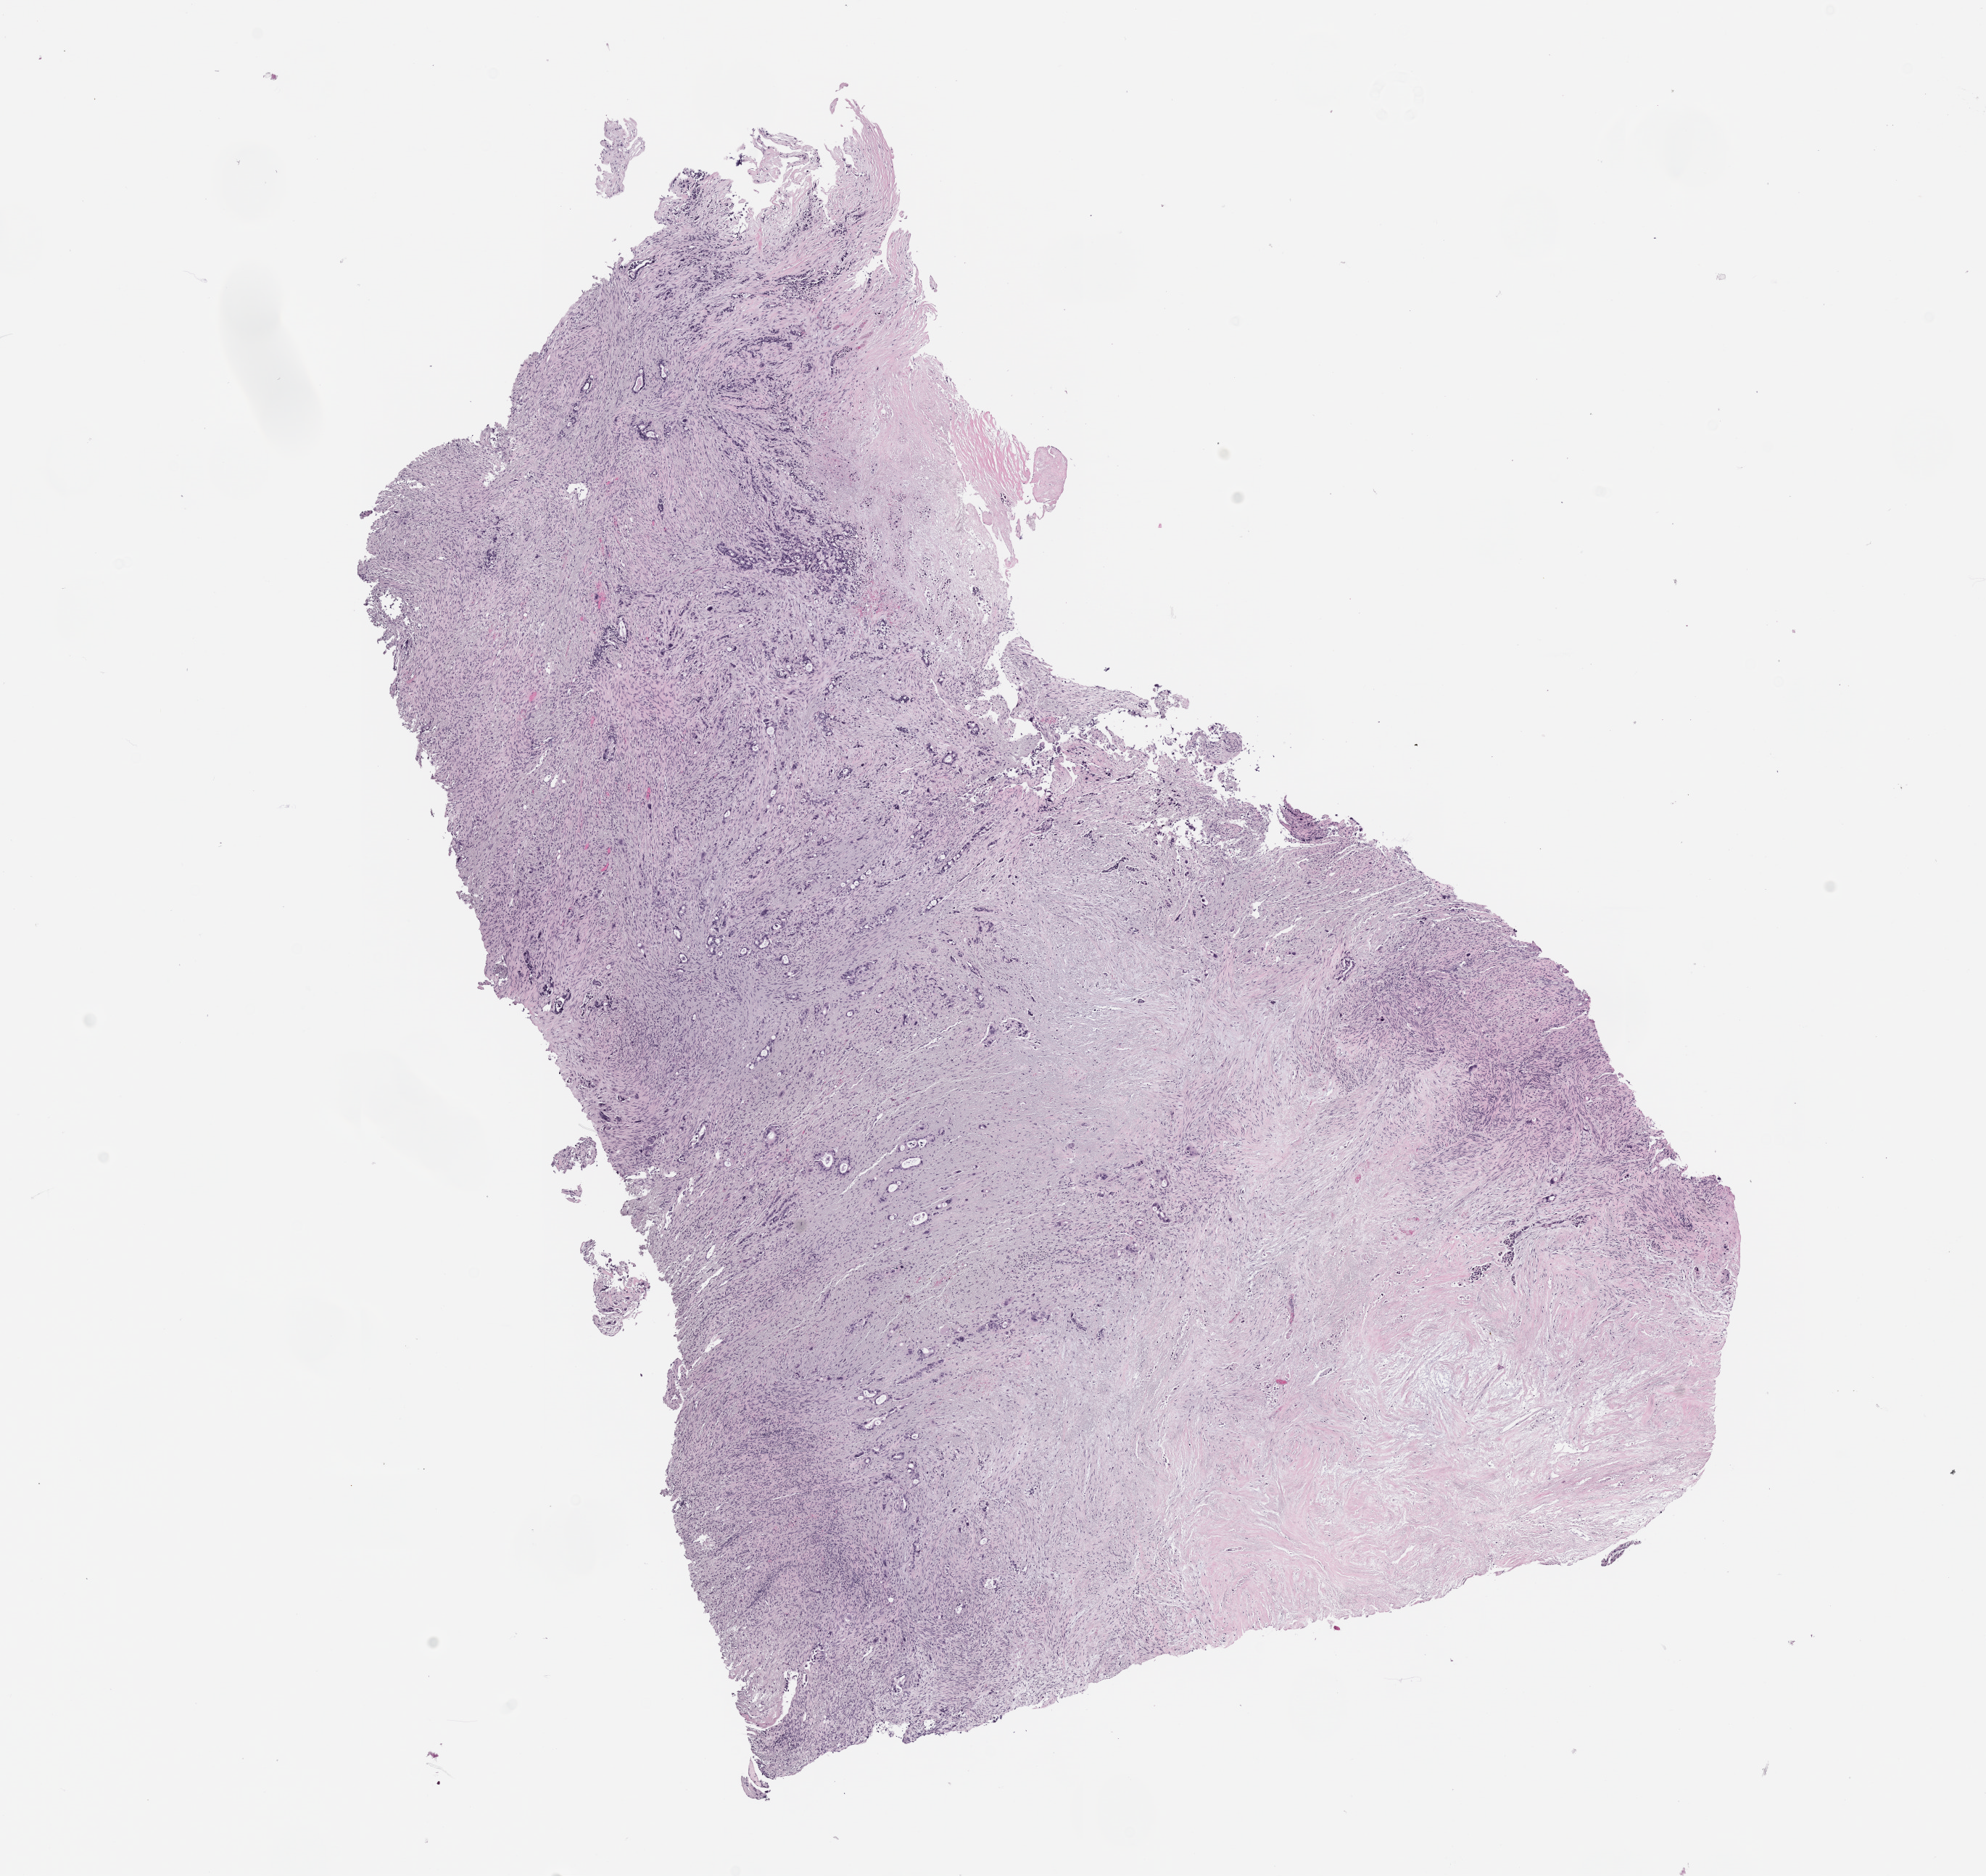
Digitized hematoxylin and eosin (H&E)-stained section of the patient's (originator) tumor tissue, a low-resolution overview of the entire scanned area, about 11.0 x 10.4 mm; formalin-fixed, paraffin-embedded (FFPE) tissue; tumor site category: pancreas. Patient female; age 62 years.
- diagnosis: Pancreatic Adenocarcinoma